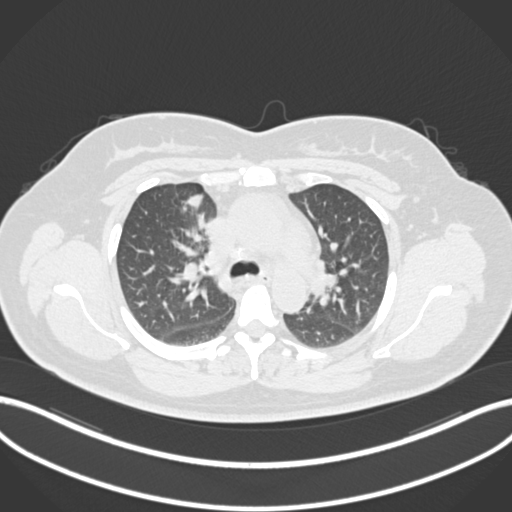
Chest CT, one axial slice. Slice 122 of 183 in the series (ordered by position). Reconstruction kernel B30f. 120 kVp. Lung window (W 1500 / L -600 HU). 1 mm slice thickness. 512 × 512 image matrix, field of view 400 × 400 mm. Patient: female, 46 years. From the clinical record (not read from this slice): clinical TNM (as recorded): T2a N1 M0.
Structures marked on this image (bounding box drawn by a radiologist):
- lung tumour (recorded histology: adenocarcinoma): bounding box (x1, y1, x2, y2) in pixels: (181, 193, 208, 235)